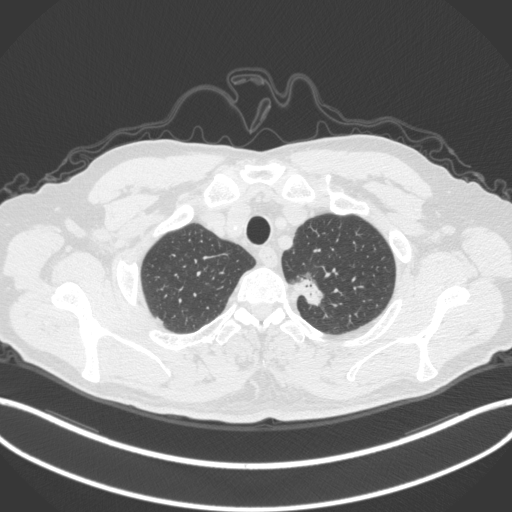
Chest CT, one axial slice; slice 334 of 382 in the series (ordered by position); 120 kVp; lung window (W 1500 / L -600 HU); 512 × 512 image matrix, field of view 400 × 400 mm. Patient: male, 64 years. Case-level facts recorded for this patient, not image findings: clinical TNM (as recorded): T1c N0 M0.
Outlined on this slice (bounding box drawn by a radiologist):
- lung tumour (recorded histology: adenocarcinoma): bounding box [x1, y1, x2, y2] px = [294, 265, 333, 307]